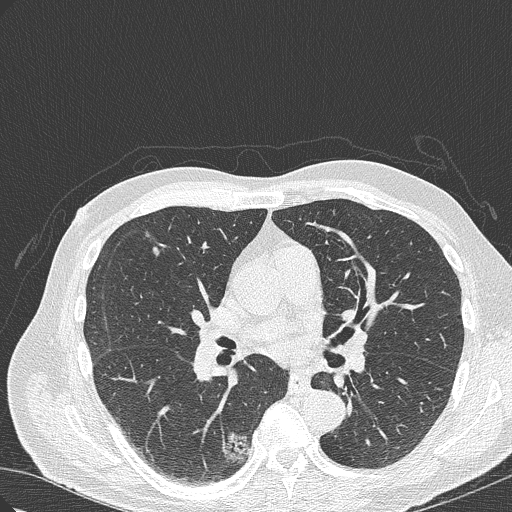
Chest CT (low-dose screening protocol), one axial image. Baseline screening round. Lung window (W 1500 / L -600 HU). 1 mm slice thickness. Lung (sharp) reconstruction kernel (B50f). Slice 145 of 322 in the series. Male participant, aged 70 years at enrolment.
Expert-annotated lung lesion, box from (x=198, y=420) to (x=261, y=480) px. The screening reader recorded 4 non-calcified nodules or masses ≥4 mm on this exam (right lower lobe, right lower lobe, right upper lobe, right lower lobe); which of them this box marks is not recorded. Official screen result: positive, change unspecified: nodule(s) >= 4 mm or enlarging nodule(s), mass(es), or other non-specific abnormalities suspicious for lung cancer. Participant outcome: lung cancer diagnosed 978 days after this screen — bronchiolo-alveolar adenocarcinoma, NOS, right lower lobe, poorly differentiated (G3), stage IB (AJCC 6th edition), 30 mm at pathology.